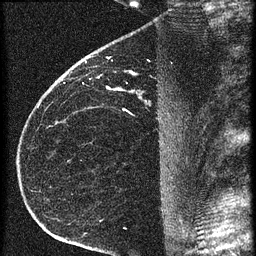
Breast MRI (dynamic contrast-enhanced), one sagittal slice. Position 42 of 60 along the scan axis. 3 images stored at this slice position (order not interpretable as contrast timing). 1.5 T. TE 4.2 ms, TR 20.4 ms. 1.5 mm slice thickness. 256 × 256 image matrix. Female patient, age 35 years. Case-level facts recorded for this patient, not image findings: setting: breast cancer imaged before/during neoadjuvant chemotherapy; receptor status: HR-positive, HER2-negative.
Structures marked on this image (semi-automatic segmentation, software-assisted and operator-edited):
- analysis volume of interest (the breast-tissue region the enhancement analysis was run in; not a lesion): bounding box [x1, y1, x2, y2] px = [65, 60, 169, 119]
- tumour enhancement mask (voxels above the 90 % enhancement threshold inside the analysis volume of interest): [85, 62, 110, 89]